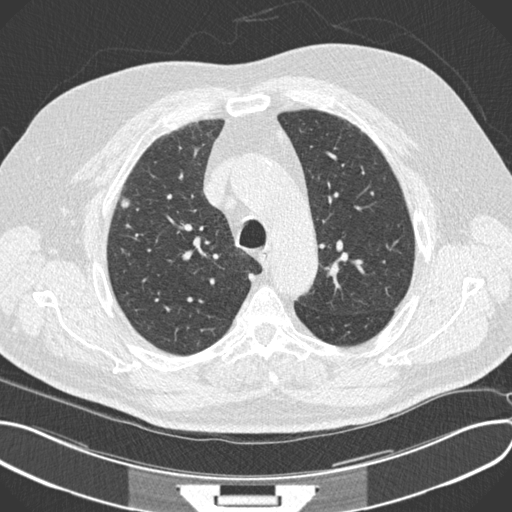
Low-dose screening chest CT, axial slice. Third annual screen. Lung window (W 1500 / L -600 HU). Standard (soft-tissue) reconstruction kernel (B30f). Male, age 64 years at enrolment. Current smoker at enrolment.
Lesion marked by an expert reader, bounding box [x1, y1, x2, y2] px = [109, 186, 141, 221]. The exam's reader record, not a measurement of the box and not confirmed to be the same lesion: non-calcified nodule or mass ≥4 mm, right upper lobe, 7 × 6 mm, smooth margins, soft tissue attenuation, pre-existing on the prior screen: no. Official screen result: positive, other. Later outcome: lung cancer diagnosed 104 days after this screen — squamous cell carcinoma, NOS, right upper lobe, moderately differentiated (G2), stage IA (AJCC 6th edition), 7 mm at pathology.